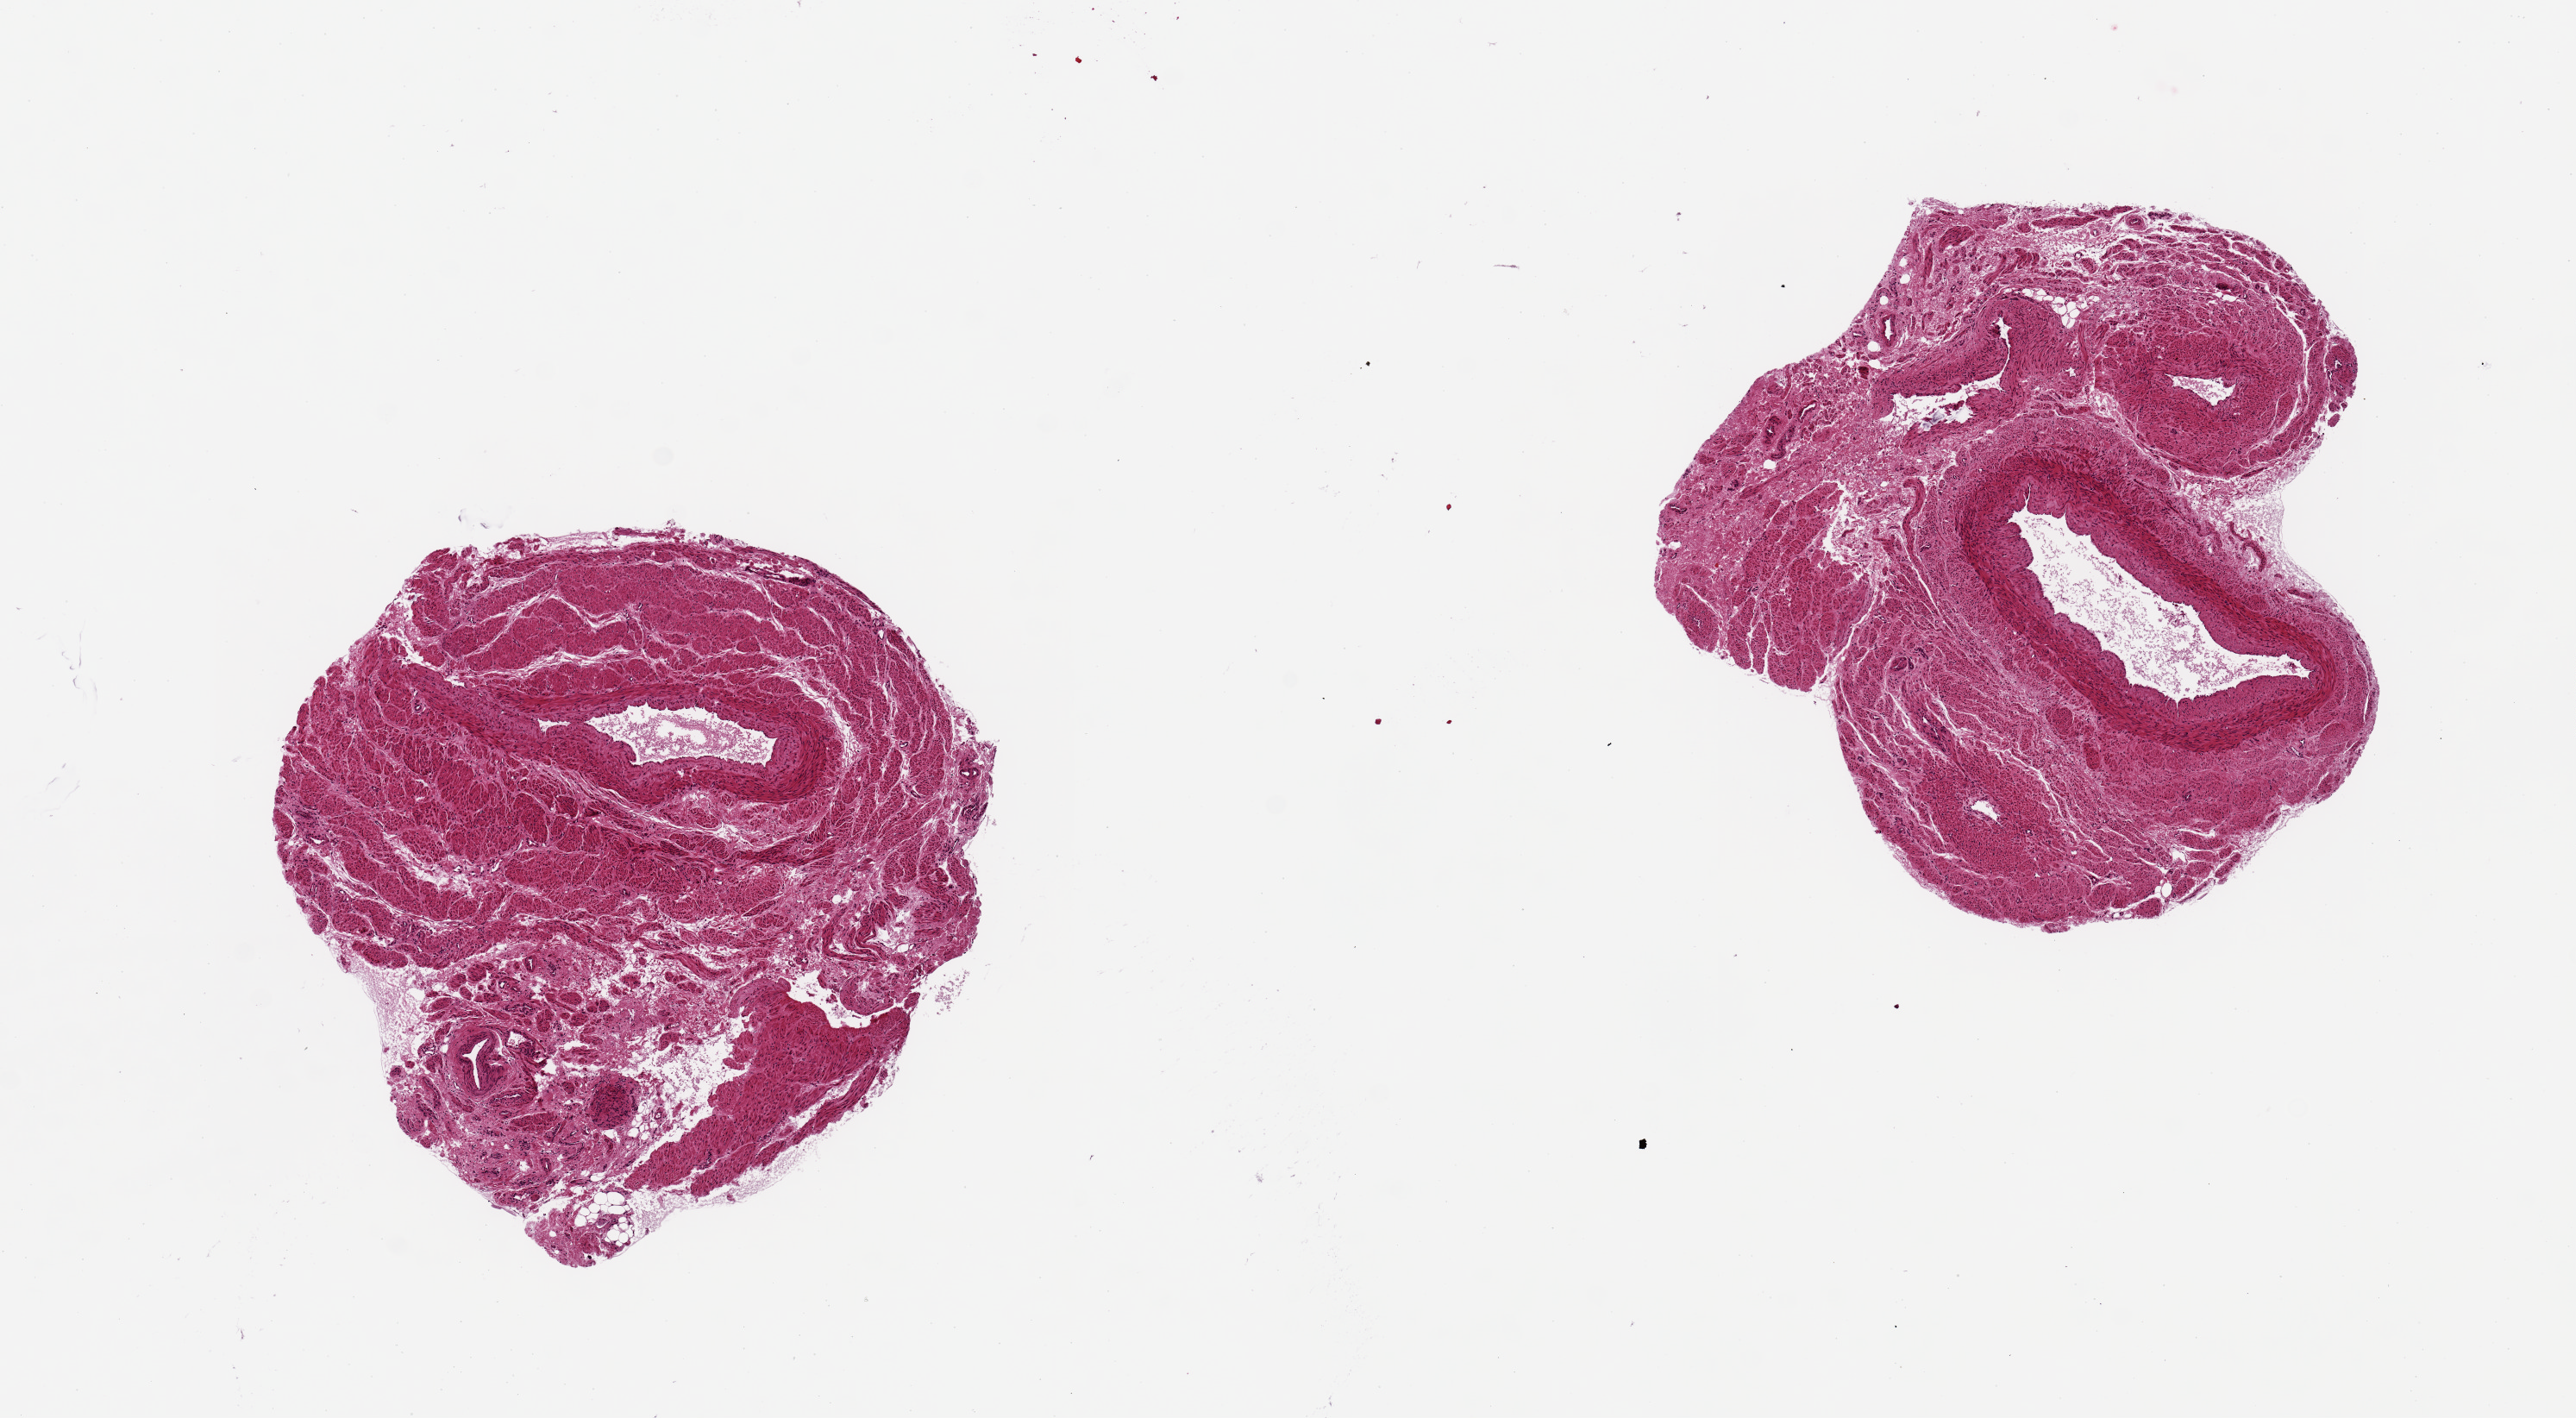
Digitized haematoxylin and eosin-stained section — shown as a low-resolution overview of the whole scanned area (about 11.8 x 6.5 mm, slide scanned at 20x). PAXgene-fixed, paraffin-embedded tissue. Section of fallopian tube (target tissue). Tissue donor sample. Female donor.
Pathologist's review note for this sample: 2 pieces fibro-vascular tissue, not tube.